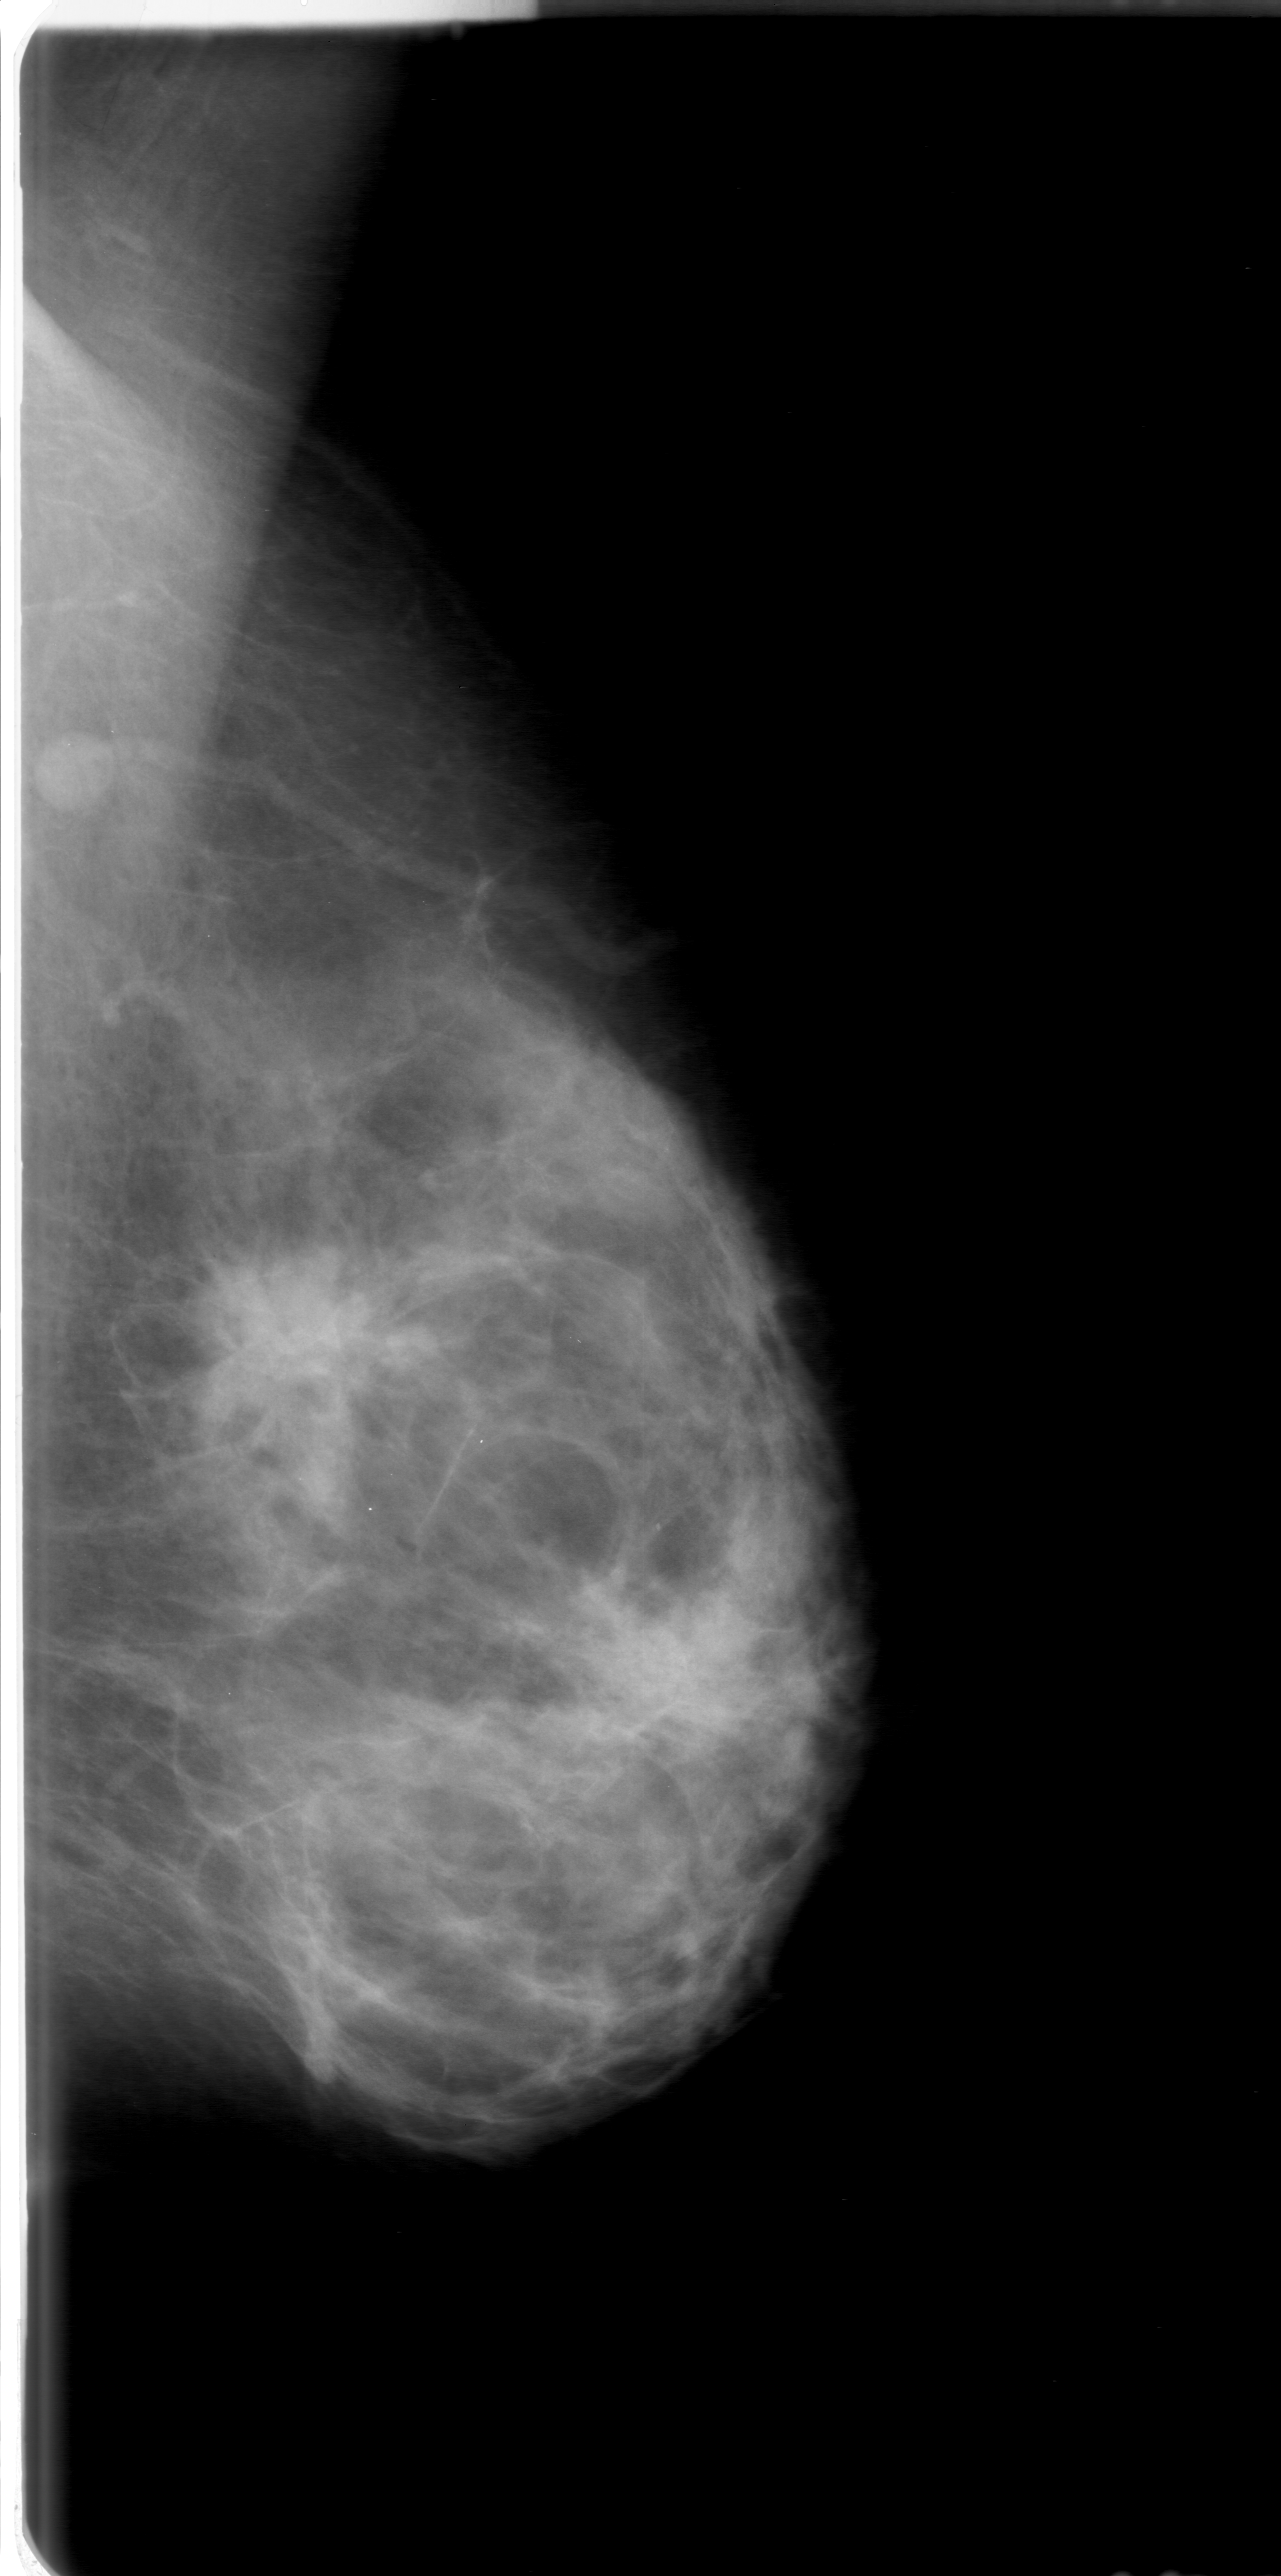
Scanned film-screen mammogram. Left breast. MLO view. Breast composition: heterogeneously dense (BI-RADS density category 3 of 4). 1281 × 2576 image matrix.
Expert-marked regions of interest on this image (one box per marked abnormality):
- mass, shape irregular, margins spiculated; BI-RADS assessment category 5; subtlety rating 4 on a 1 (subtle) to 5 (obvious) scale; pathology result (as recorded, not read from the image): malignant: bounding box <207,1239,417,1456> (left, top, right, bottom; pixels)